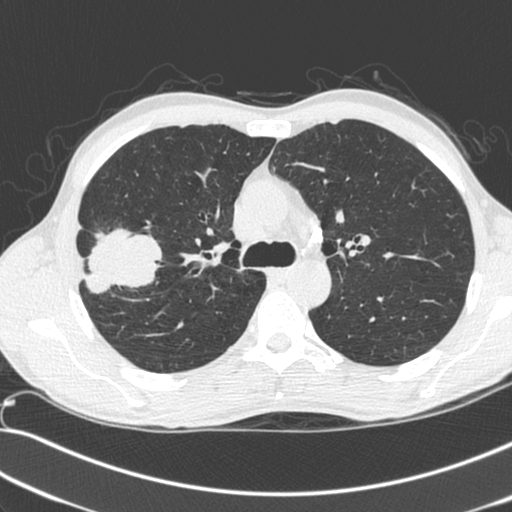
Low-dose screening chest CT, axial slice, first (baseline) screen, lung window (W 1500 / L -600 HU), 1.3 mm slice thickness, slice 80 of 281 in the series, 512 × 512 image matrix. Male participant, aged 55 years at enrolment.
Expert reader's lesion annotation, bounding box (x1, y1, x2, y2) in pixels: (70, 229, 153, 303). The exam's reader record, not a measurement of the box and not confirmed to be the same lesion: non-calcified nodule or mass ≥4 mm, right upper lobe, 52 × 39 mm, spiculated (stellate) margins, soft tissue attenuation. Official screen result: positive, change unspecified: nodule(s) >= 4 mm or enlarging nodule(s), mass(es), or other non-specific abnormalities suspicious for lung cancer. Later outcome: lung cancer diagnosed 25 days after this screen — large cell neuroendocrine carcinoma, right upper lobe, poorly differentiated (G3), stage IIB (AJCC 6th edition), 49 mm at pathology.